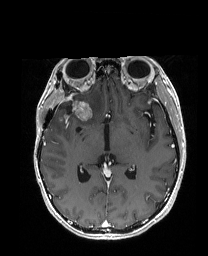
Brain MRI from a brain-tumour surgery series, one axial slice; slice 98 of 192 in the series (ordered by position); T1-weighted post-contrast; 208 × 256 image matrix, field of view 203 × 250 mm. Case-level facts recorded for this patient, not image findings: histopathology: Metastatic Carcinoma from Breast primary; tumour location: Right Frontal.
Structures marked on this image (manually delineated by an expert):
- previous resection cavity: bounding box (x1, y1, x2, y2) in pixels: (60, 105, 71, 113)
- tumour: (55, 99, 104, 121)